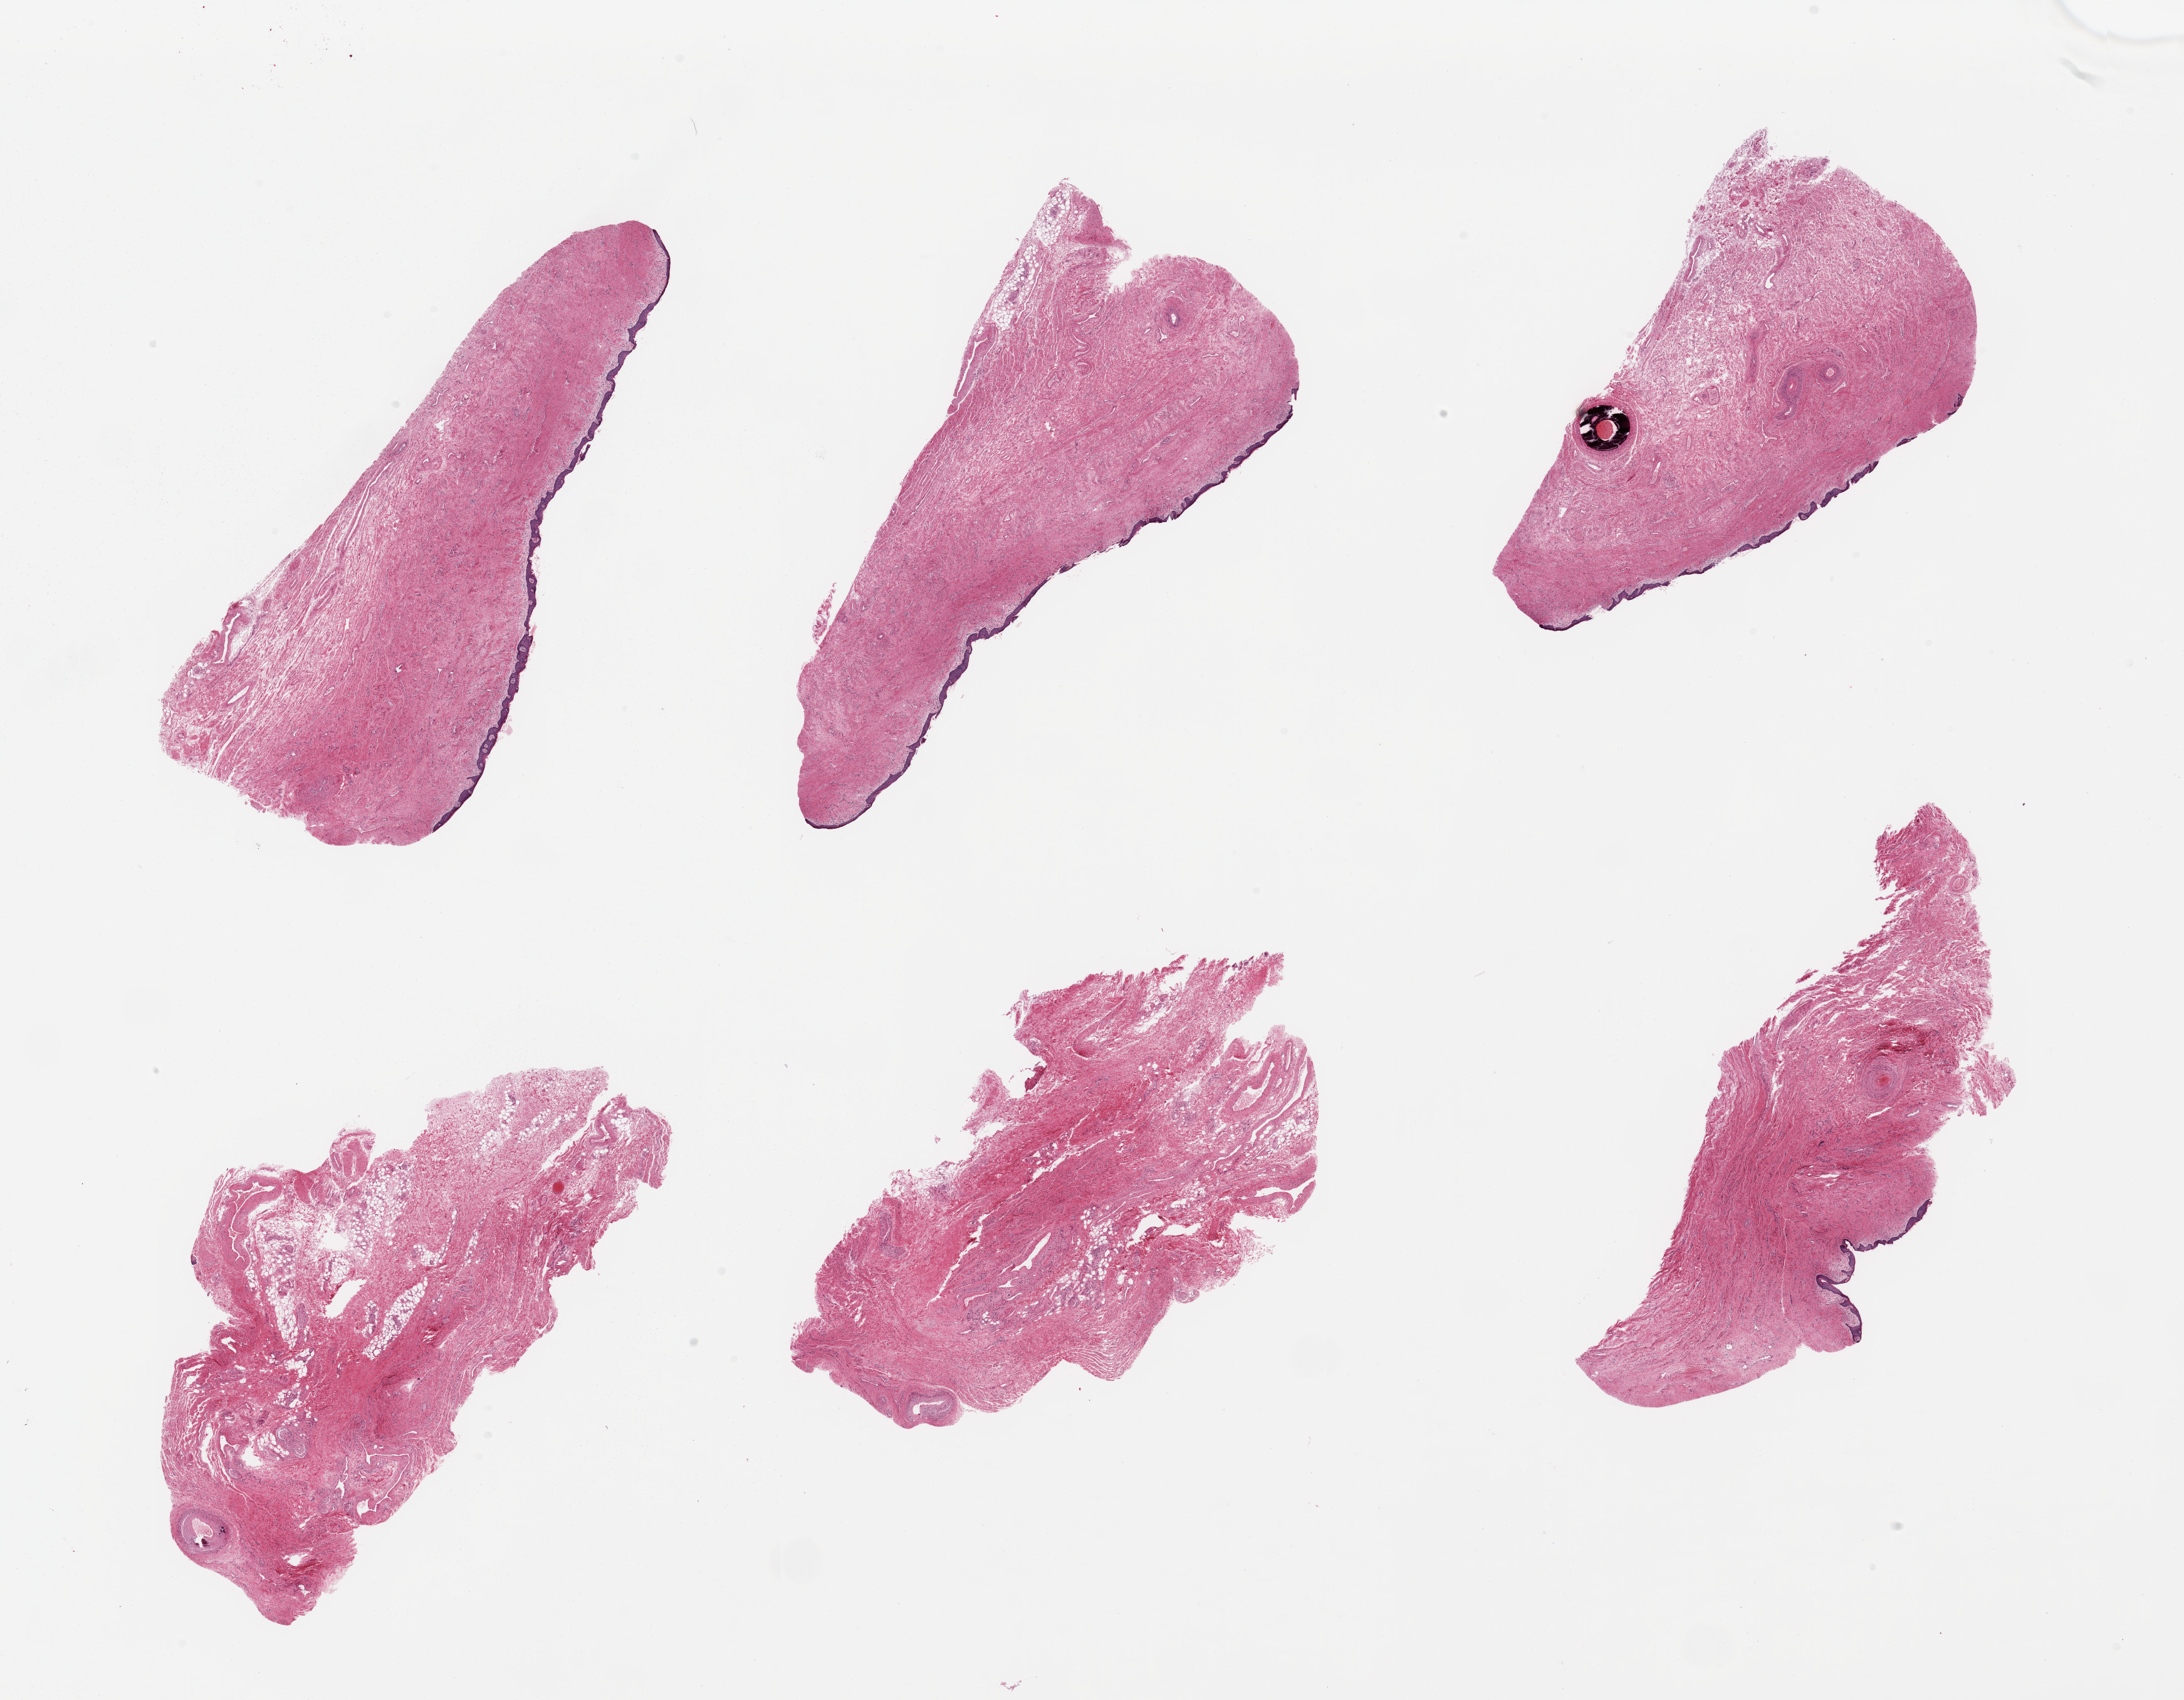
Whole-slide image, H&E stain, brightfield — whole scanned area (about 27.6 x 21.5 mm, acquisition: 20x scan) shown as a low-resolution overview; PAXgene-fixed, paraffin-embedded tissue; section of vagina (target tissue); tissue donor sample. Donor sex: female.
Reviewer comment on this tissue sample: 6 pieces, squamous mucosa up to ~0.1mm.